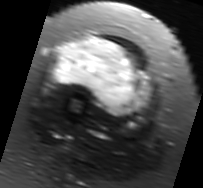
MRI of an extremity soft-tissue mass, one axial slice; slice 28 of 91 in the series (ordered by position); T2-weighted fat-saturated; MR volume resampled by the dataset authors to the PET/CT grid (not the native acquisition matrix); 3.27 mm slice thickness; 203 × 188 image matrix, field of view 198 × 184 mm. Female patient. Case-level facts recorded for this patient, not image findings: histological type: malignant solitary fibrous tumor; grade: intermediate; site of the primary tumour: right thigh.
Outlined on this slice (expert contour drawn on MRI and transferred to this co-registered scan by the dataset authors):
- gross tumour volume including surrounding oedema: bounding box [x1, y1, x2, y2] px = [53, 37, 155, 121]
- gross tumour volume (mass): [56, 38, 150, 111]